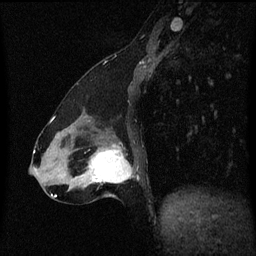
Breast MRI (dynamic contrast-enhanced), one sagittal slice; slice 21 of 60 in the series (ordered by position); dynamic contrast-enhanced series, image 2 of 3 at this slice position (ordered by acquisition); 1.5 T; TE 4.2 ms, TR 8.4 ms; 256 × 256 image matrix, field of view 200 × 200 mm. Female patient, age 47 years.
Structures marked on this image (semi-automatic segmentation, software-assisted and operator-edited):
- analysis volume of interest (the breast-tissue region the enhancement analysis was run in; not a lesion): bounding box [x1, y1, x2, y2] px = [81, 140, 135, 197]
- tumour enhancement mask (voxels above the 70 % enhancement threshold inside the analysis volume of interest): [89, 146, 132, 183]